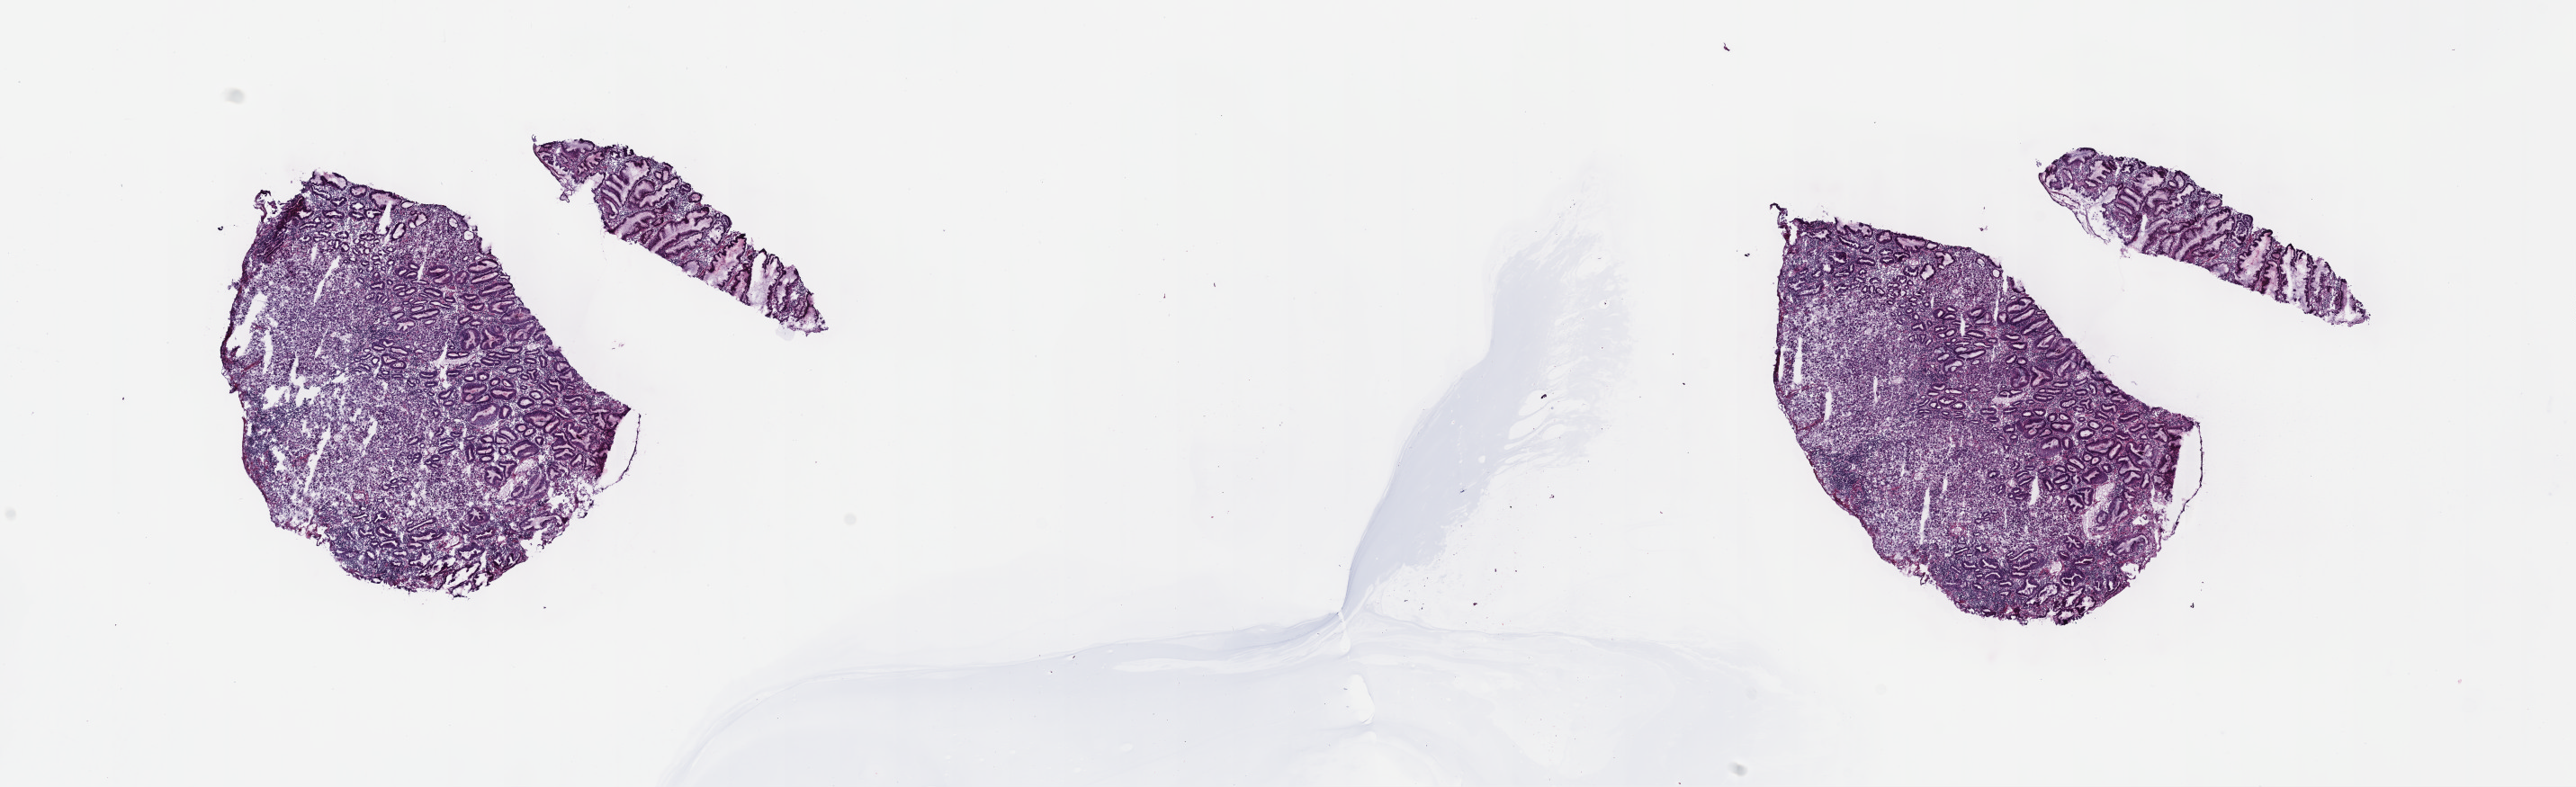
Digitized Hematoxylin and eosin (H&E) stained tissue section (whole slide), a low-resolution overview of the entire scanned area, about 23.2 x 7.1 mm (acquisition: 40x scan), frozen section from the top of the tissue portion, primary tumour sample from the stomach. Male patient; age at initial diagnosis 60 years. Histologic grade: G3 (poorly differentiated). Composition of this section per pathologist review: tumour cells 70%, tumour nuclei 70%, normal cells 10%, stromal cells 20%, necrosis 0%. Infiltration values recorded for this section: lymphocyte infiltration 40%, monocyte infiltration 20%, neutrophil infiltration 20%.
* AJCC pathologic stage: IIIC (7th edition)
* histologic diagnosis: Signet ring cell carcinoma (body of stomach)
* lymph nodes positive (case pathology): 15 of 25 examined